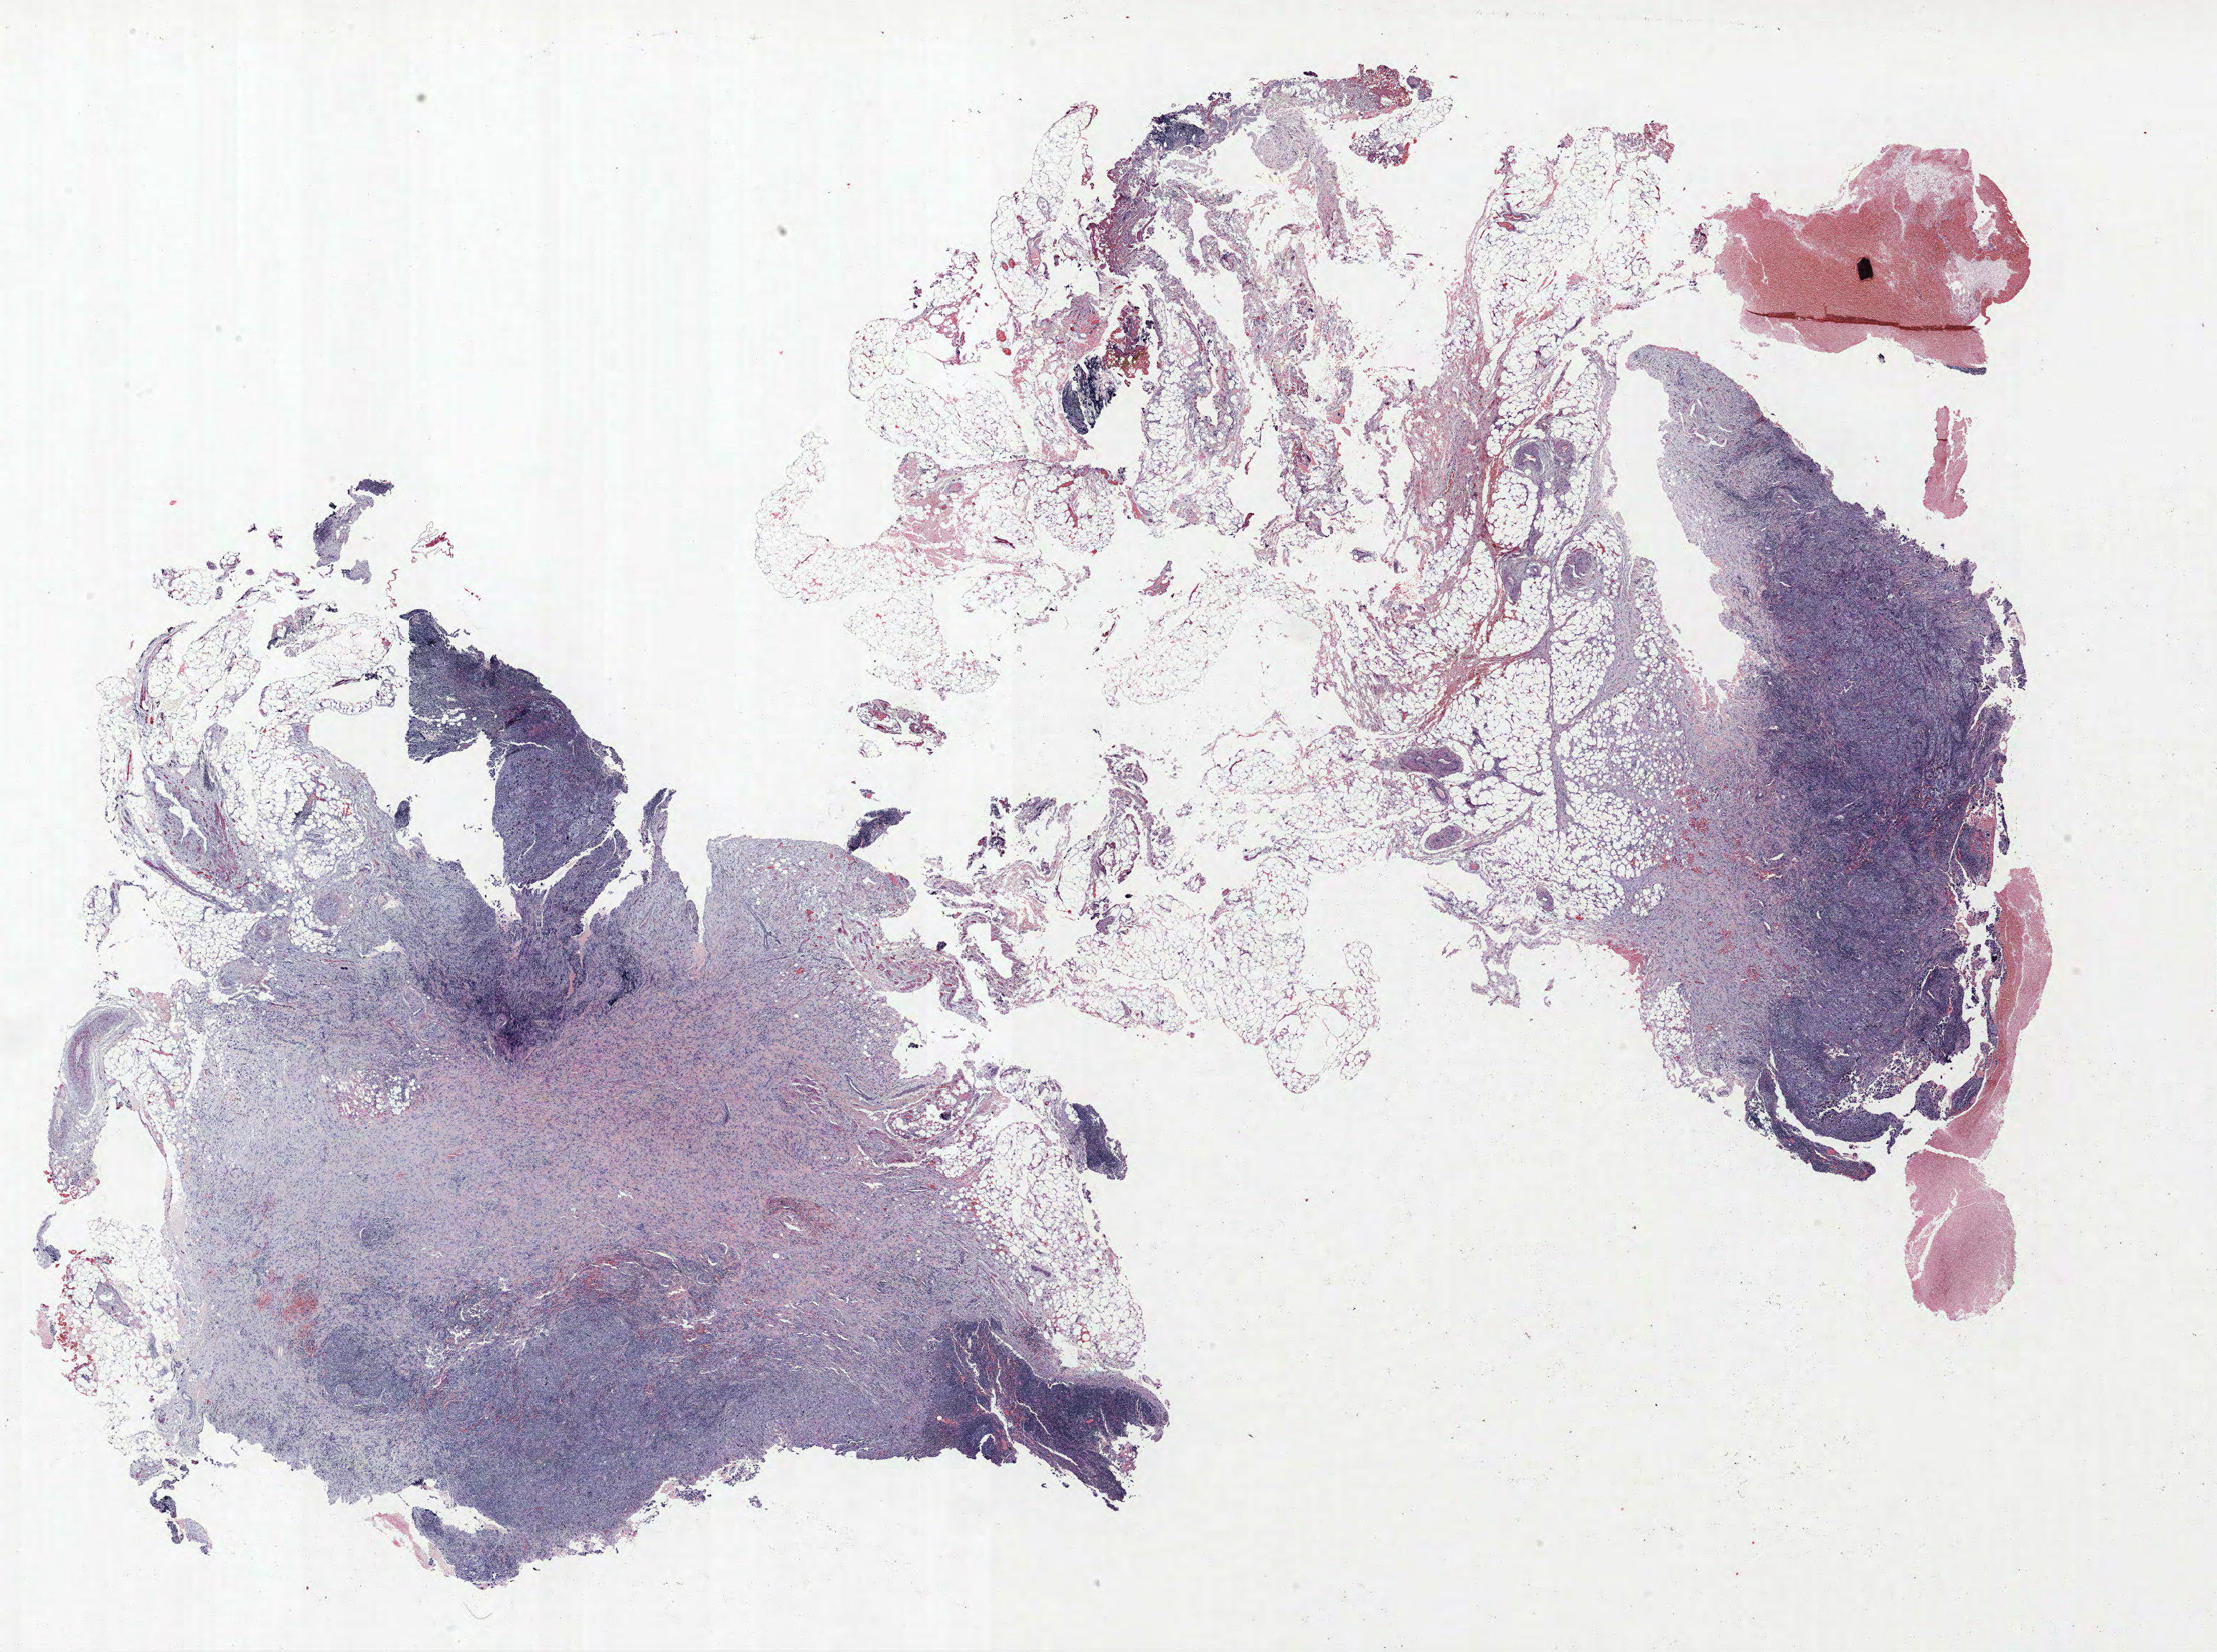
Hematoxylin and eosin (H&E) stained whole-slide image — a low-resolution overview of the entire scanned area, about 24.7 x 18.4 mm (from a 40x scan). FFPE section. Lung tissue. Male, age 61 at enrolment. Grade: well differentiated (G1).
Participant's lung-cancer diagnosis: Adenocarcinoma, NOS. ICD-O-3 topography: upper lobe of lung (C34.1). Primary tumour location (clinical record): left upper lobe. Stage (AJCC 6th edition): IIIA. Tumour size (pathology): 45 mm.